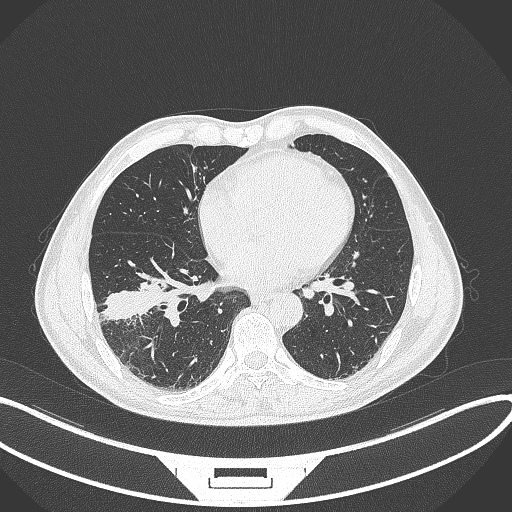
Chest CT, one axial slice. Position 144 of 364 along the scan axis. 120 kVp. Lung window (W 1500 / L -600 HU). 1 mm slice thickness. 512 × 512 image matrix, field of view 400 × 400 mm. Male patient, age 58 years. From the clinical record (not read from this slice): clinical TNM (as recorded): T3 N0 M0.
Structures marked on this image (bounding box drawn by a radiologist):
- lung tumour (recorded histology: squamous cell carcinoma): bounding box (x1, y1, x2, y2) in pixels: (103, 278, 168, 323)